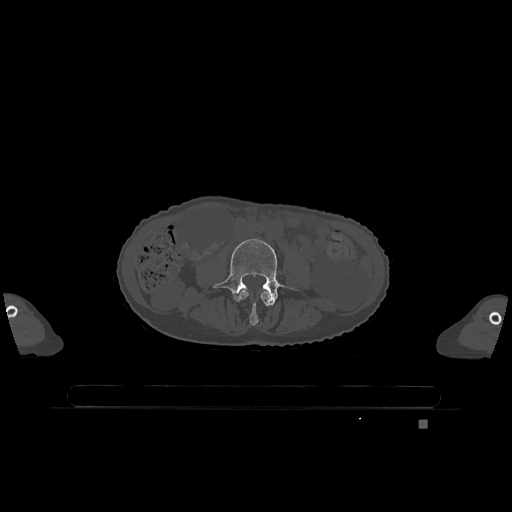
CT including the spine, one axial slice; slice 314 of 1317 in the series (ordered by position); bone window (W 1800 / L 400 HU); 0.5 mm slice thickness; 512 × 512 image matrix, field of view 500 × 500 mm. Female patient, age 74 years. Case-level facts recorded for this patient, not image findings: primary cancer: lung.
Outlined on this slice (semi-automatic segmentation, software-assisted and operator-edited):
- L3 vertebra: bounding box (x1, y1, x2, y2) in pixels: (239, 290, 271, 326)
- L4 vertebra: (213, 238, 294, 305)